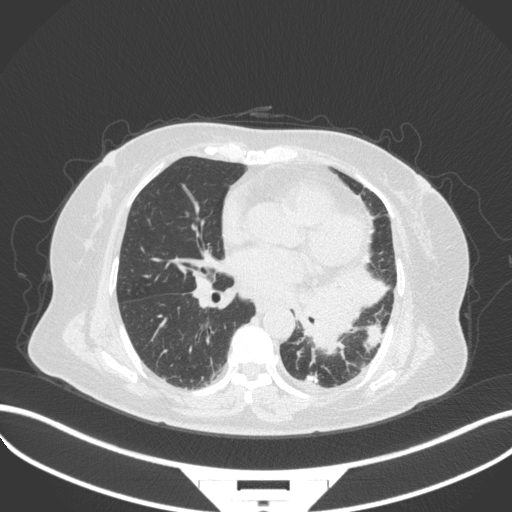
Chest CT, one axial slice; position 164 of 328 along the scan axis; 120 kVp; lung window (W 1500 / L -600 HU); 1 mm slice thickness; 512 × 512 image matrix, field of view 400 × 400 mm. Patient: female, 69 years. From the clinical record (not read from this slice): clinical TNM (as recorded): T2b N3 M1.
Structures marked on this image (rectangle marked by the reading radiologist):
- lung tumour (recorded histology: adenocarcinoma): bounding box (x1, y1, x2, y2) in pixels: (289, 258, 390, 356)